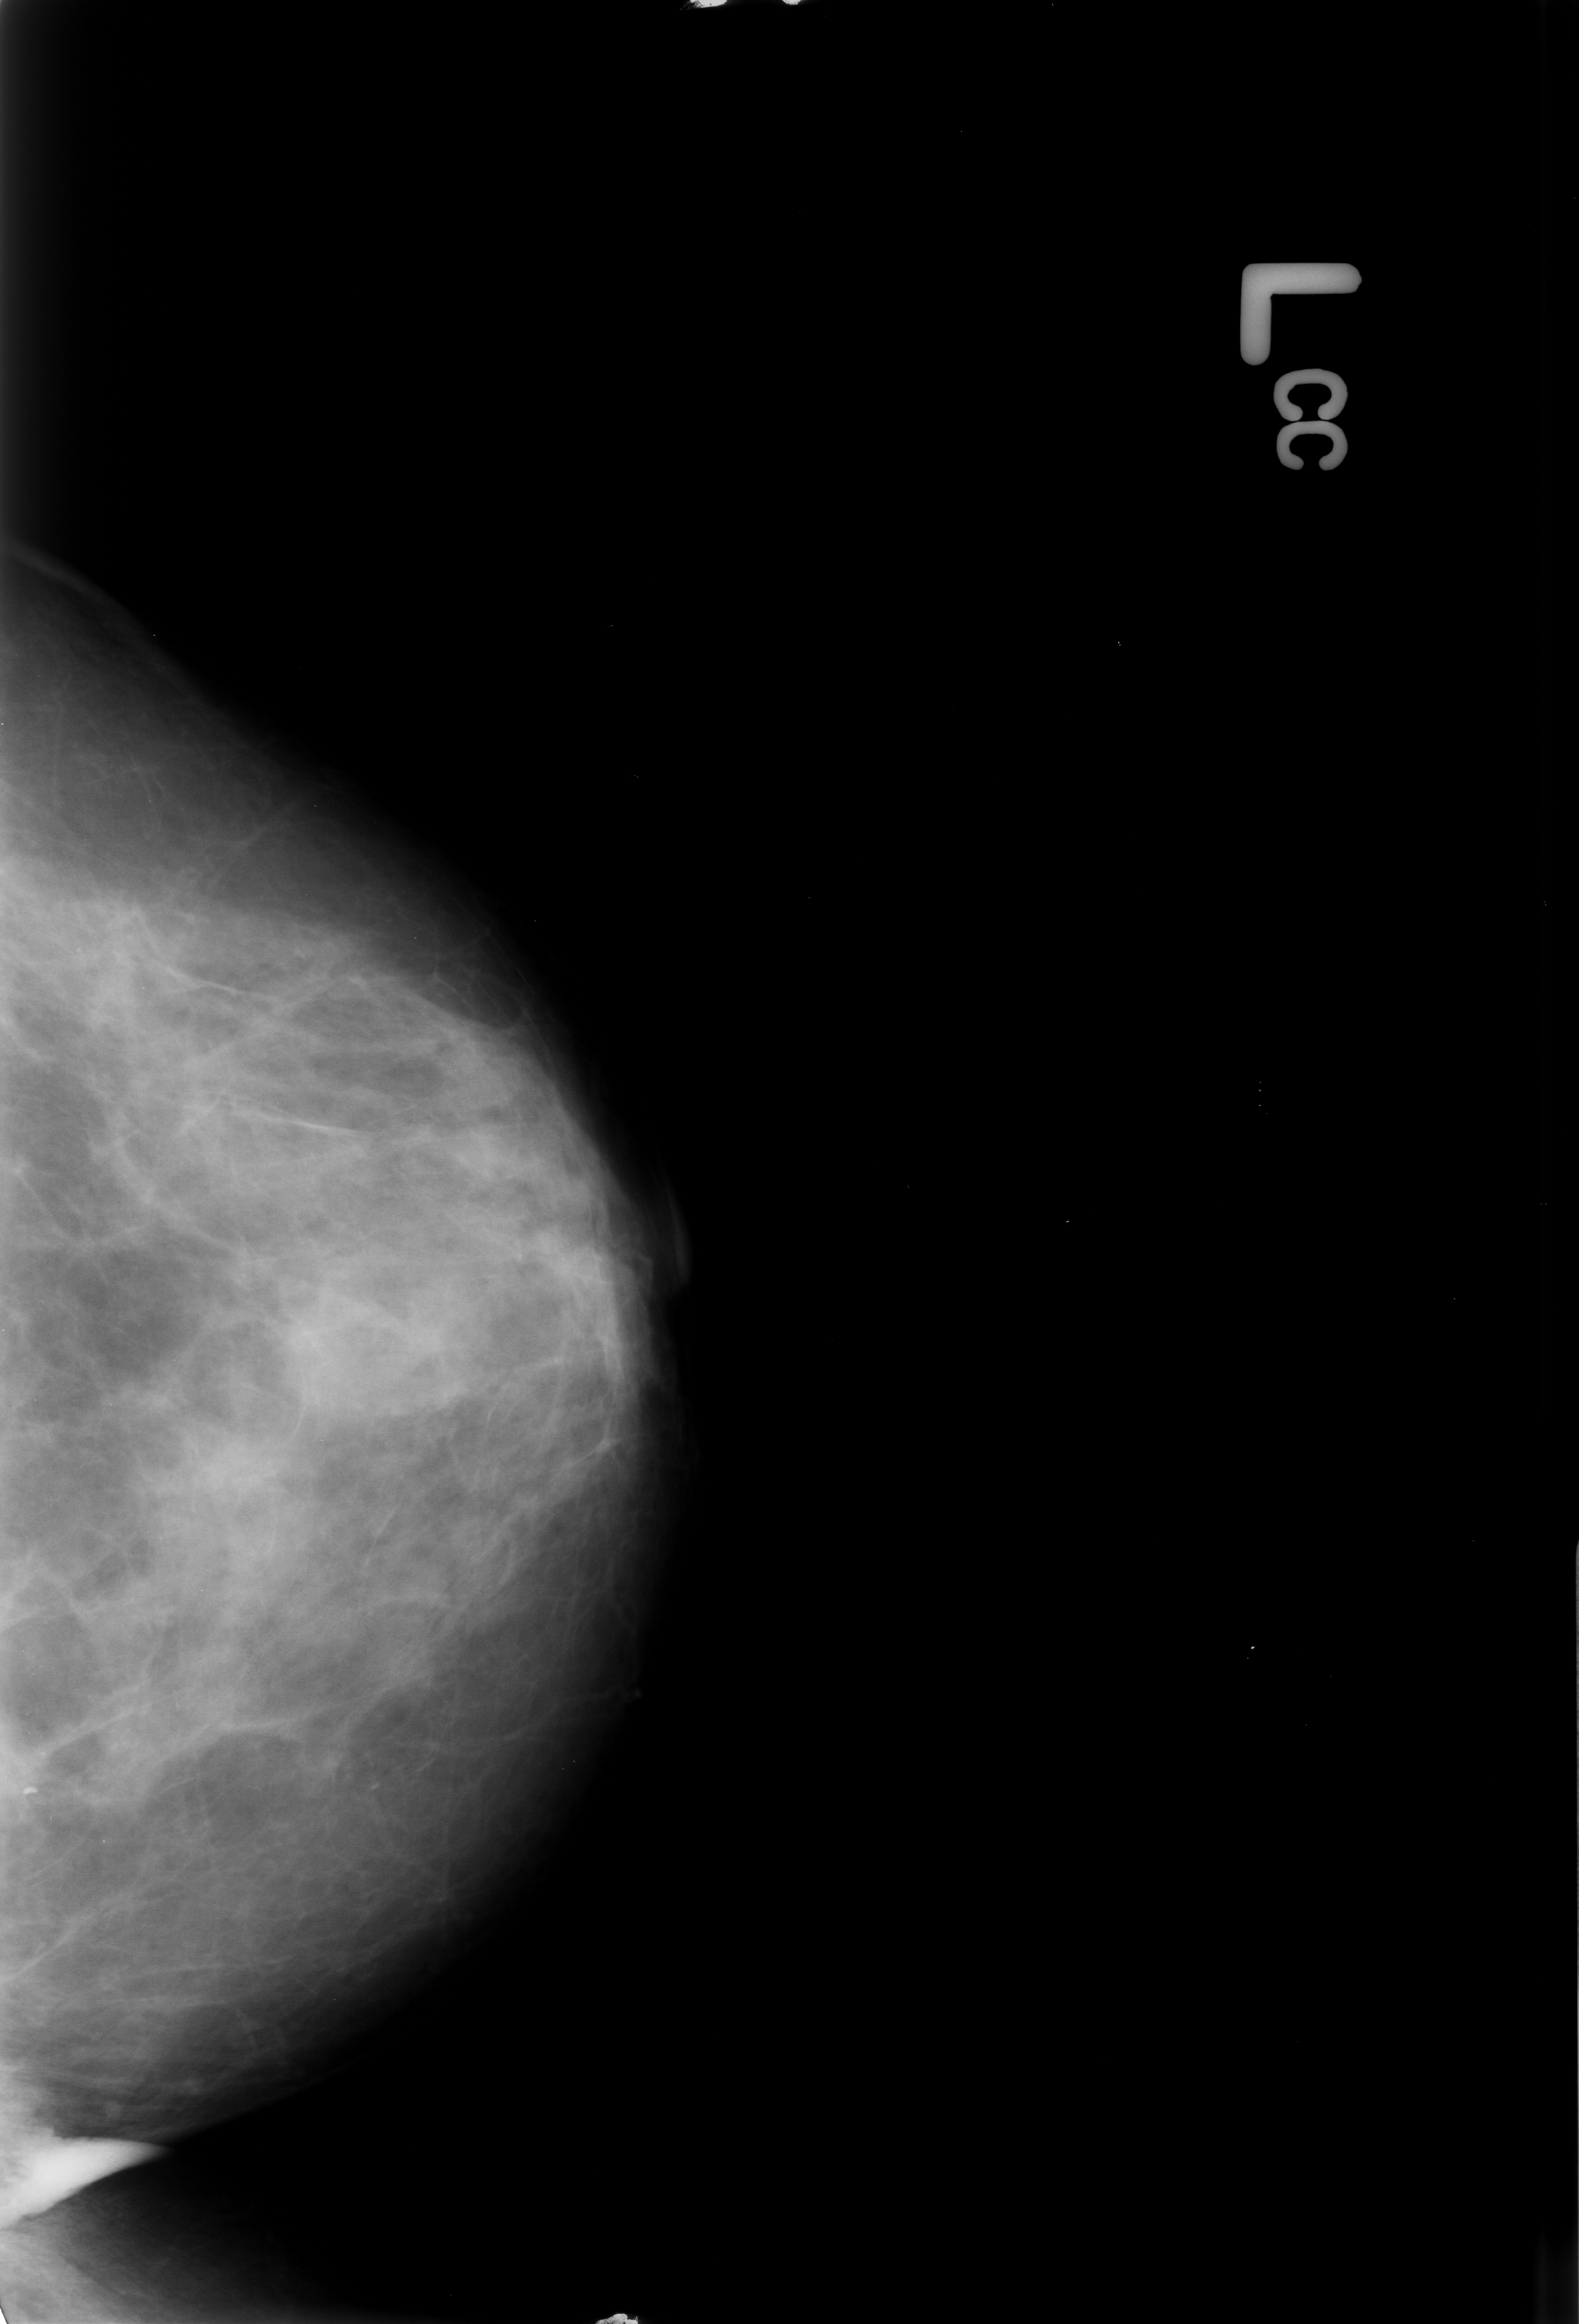
Scanned film-screen mammogram. Left breast. Craniocaudal (CC) view. 1579 × 2324 image matrix.
Expert-marked regions of interest on this film, with their recorded descriptors:
- calcifications, morphology pleomorphic, distribution clustered; BI-RADS assessment category 4; pathology (as recorded): malignant: bounding box (x1, y1, x2, y2) in pixels: (0, 1681, 71, 1839)